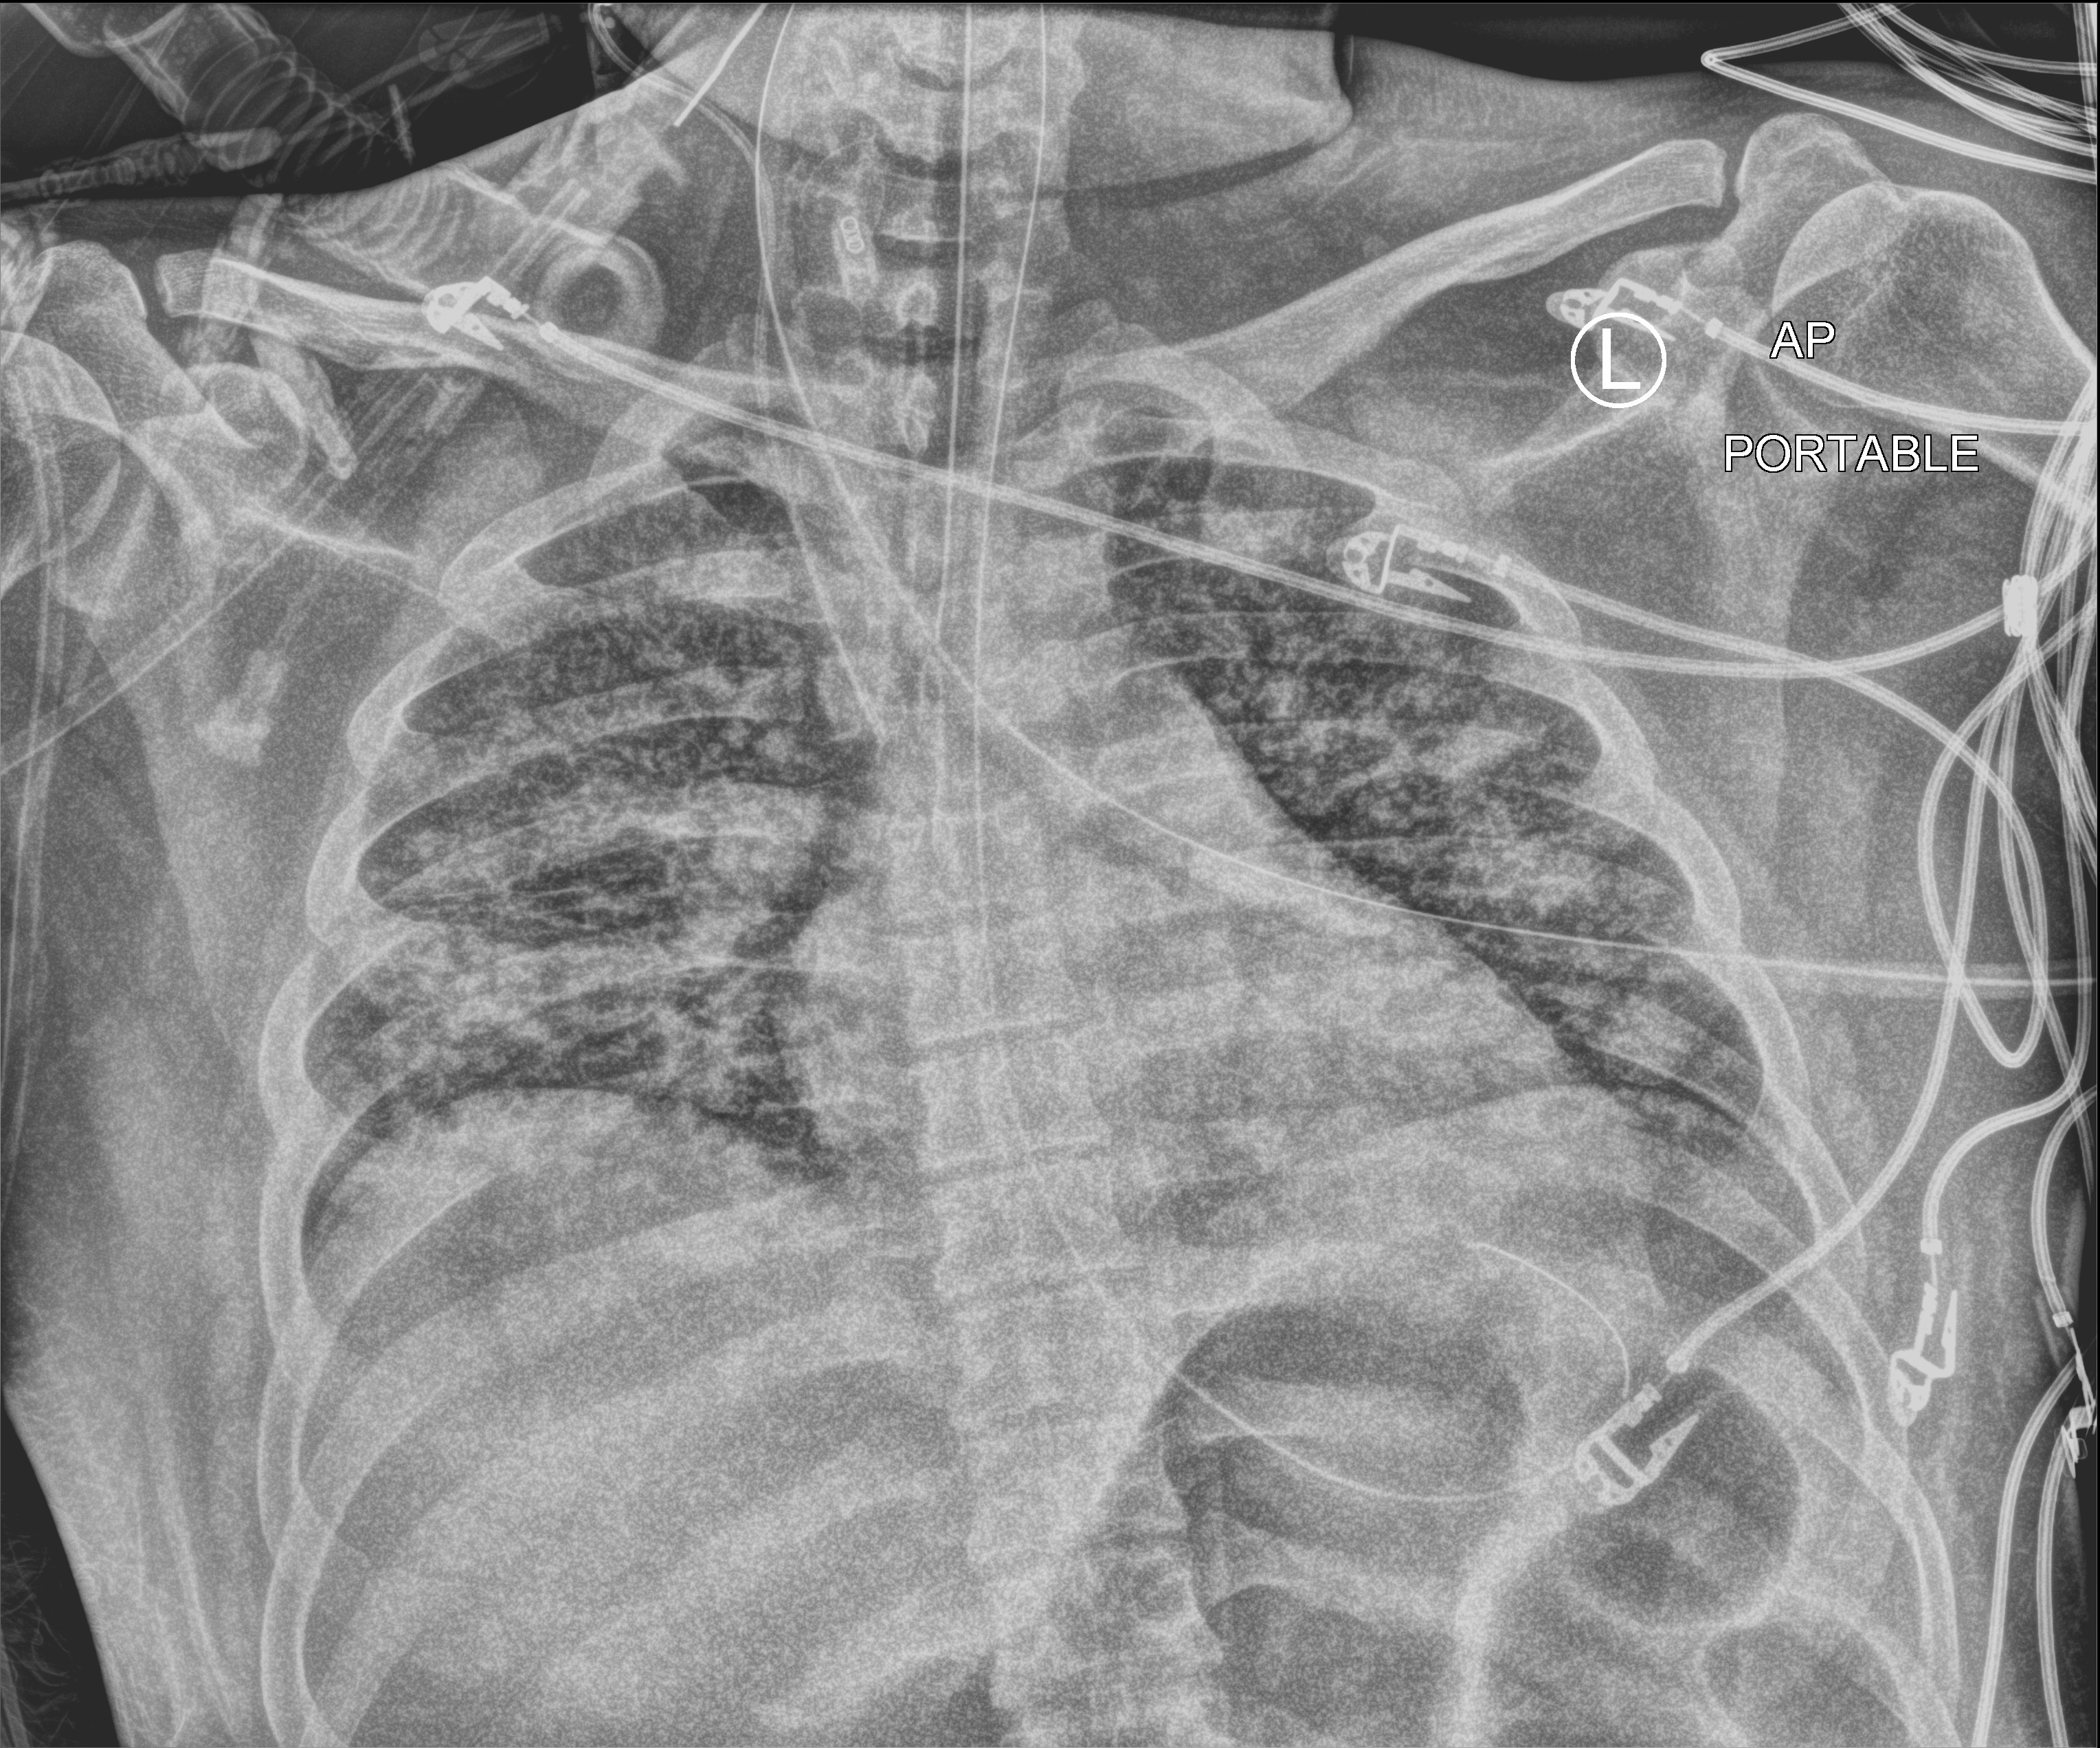
Portable chest radiograph, anteroposterior (AP) projection. Patient hospitalised with COVID-19; male, aged 18–59 years.
Hospital-stay facts (about this admission, not read from this image; timing relative to this image not recorded): admitted to intensive care during this hospital stay: yes.